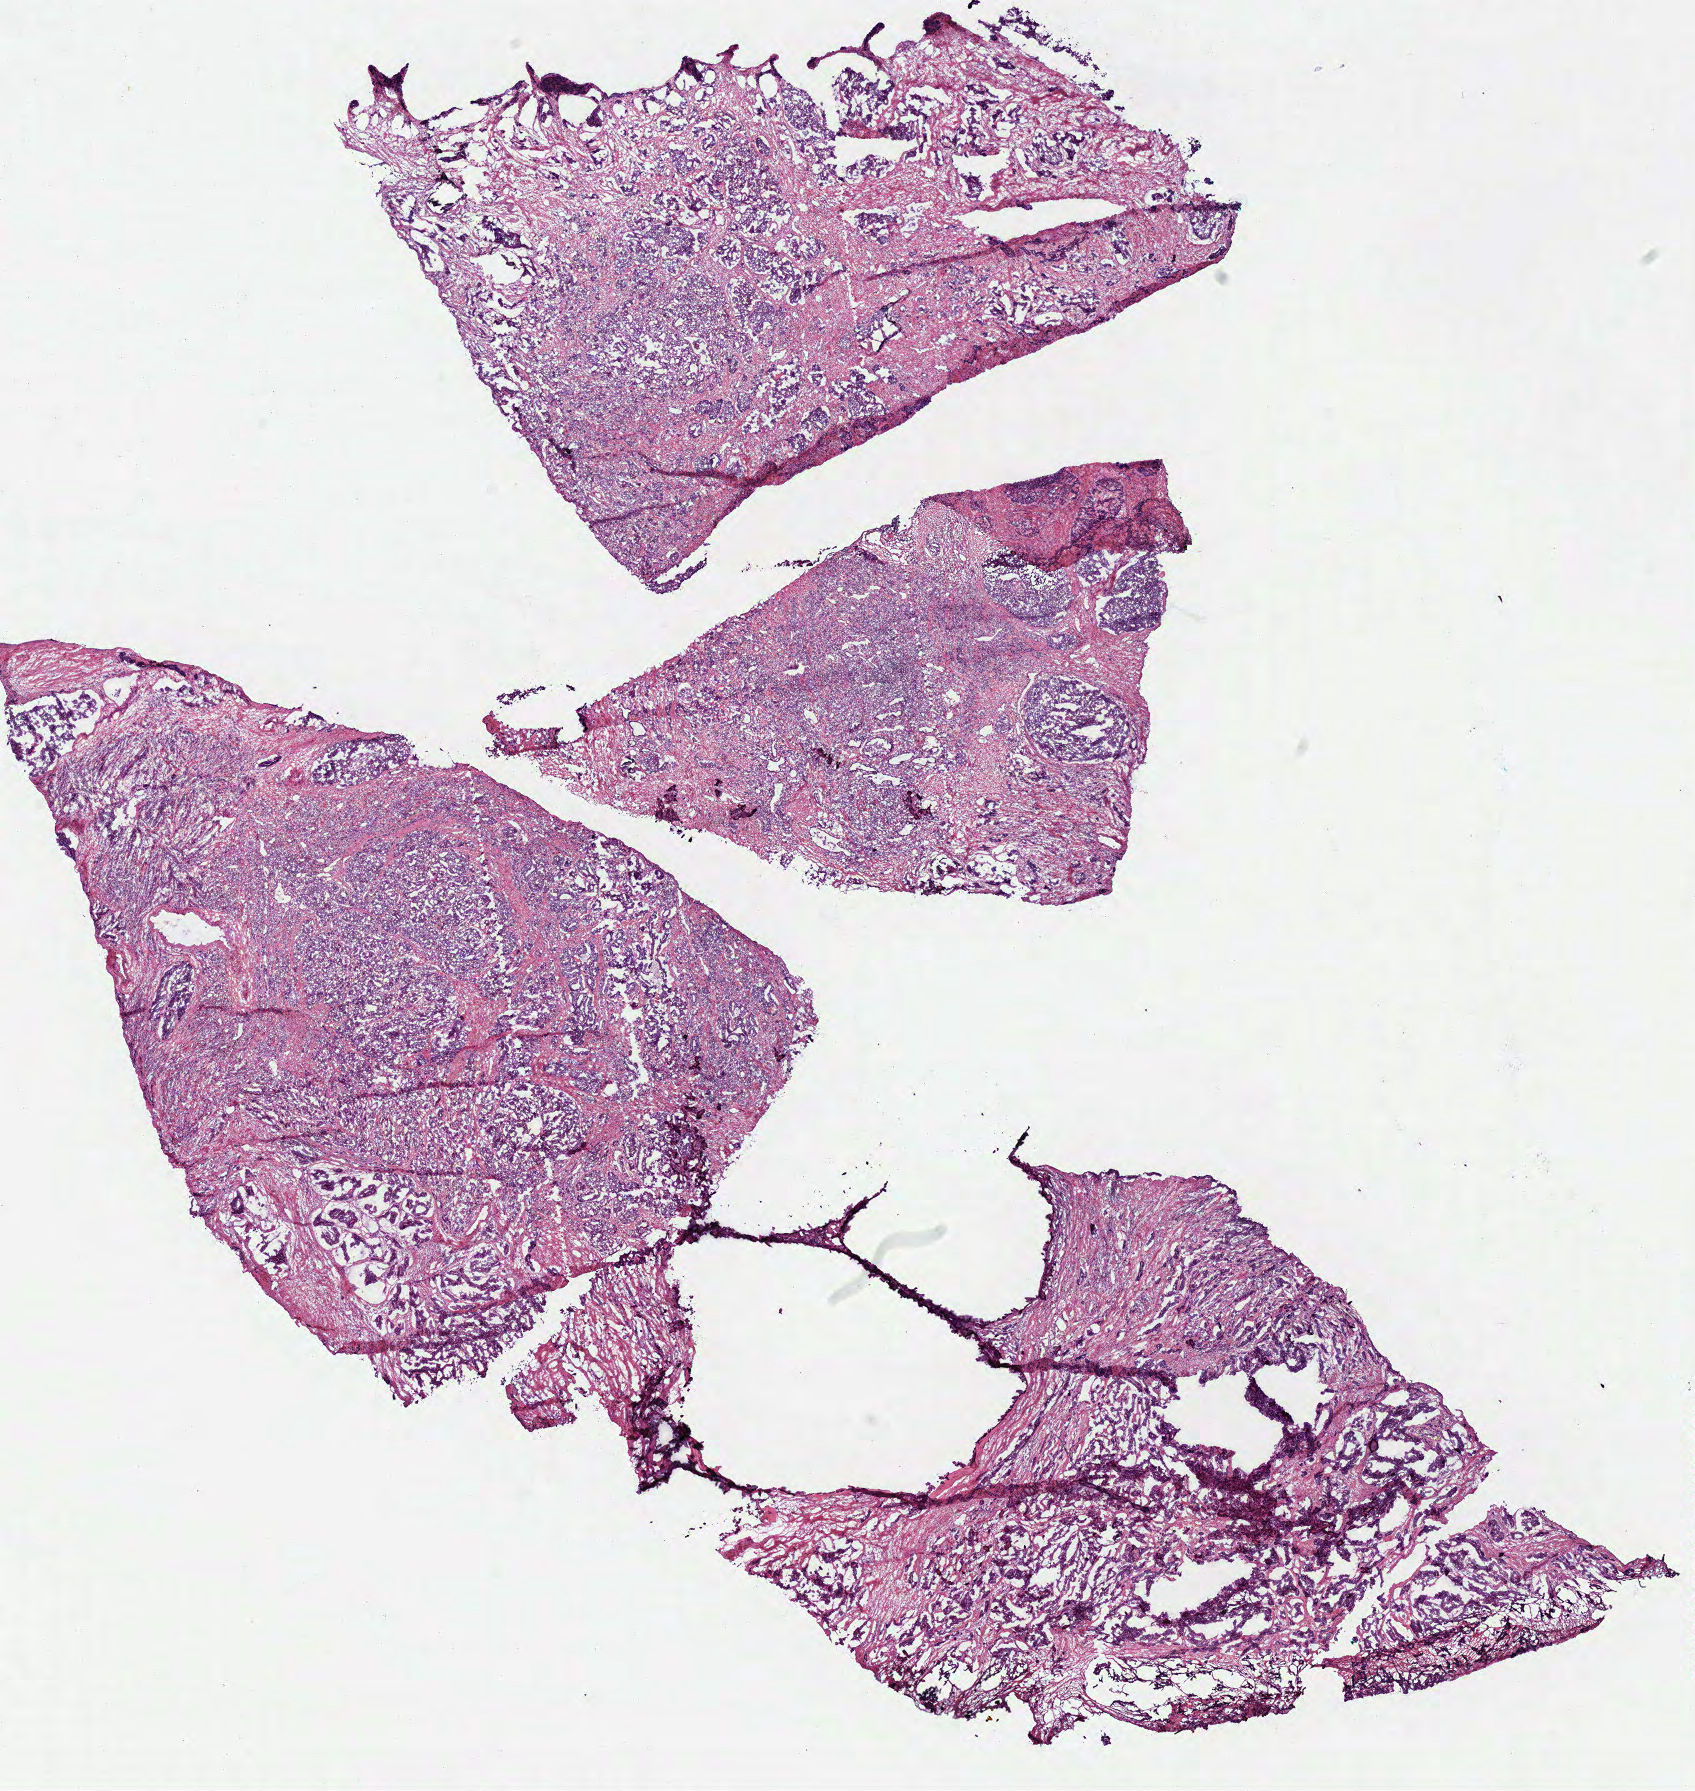
Whole-slide histology image, H&E — low-resolution overview of the scanned area, about 13.4 x 14.1 mm; frozen section from the top of the tissue portion; prostate, primary tumour sample. Male, age 56 years at initial diagnosis. Gleason score: 9 (5+4). Composition of this section per pathologist review: tumour cells 80%, tumour nuclei 75%, normal cells 0%, stromal cells 20%, necrosis 0%.
Diagnosis: Acinar cell carcinoma (prostate gland). Lymph nodes positive (case pathology): 0 of 7 examined.